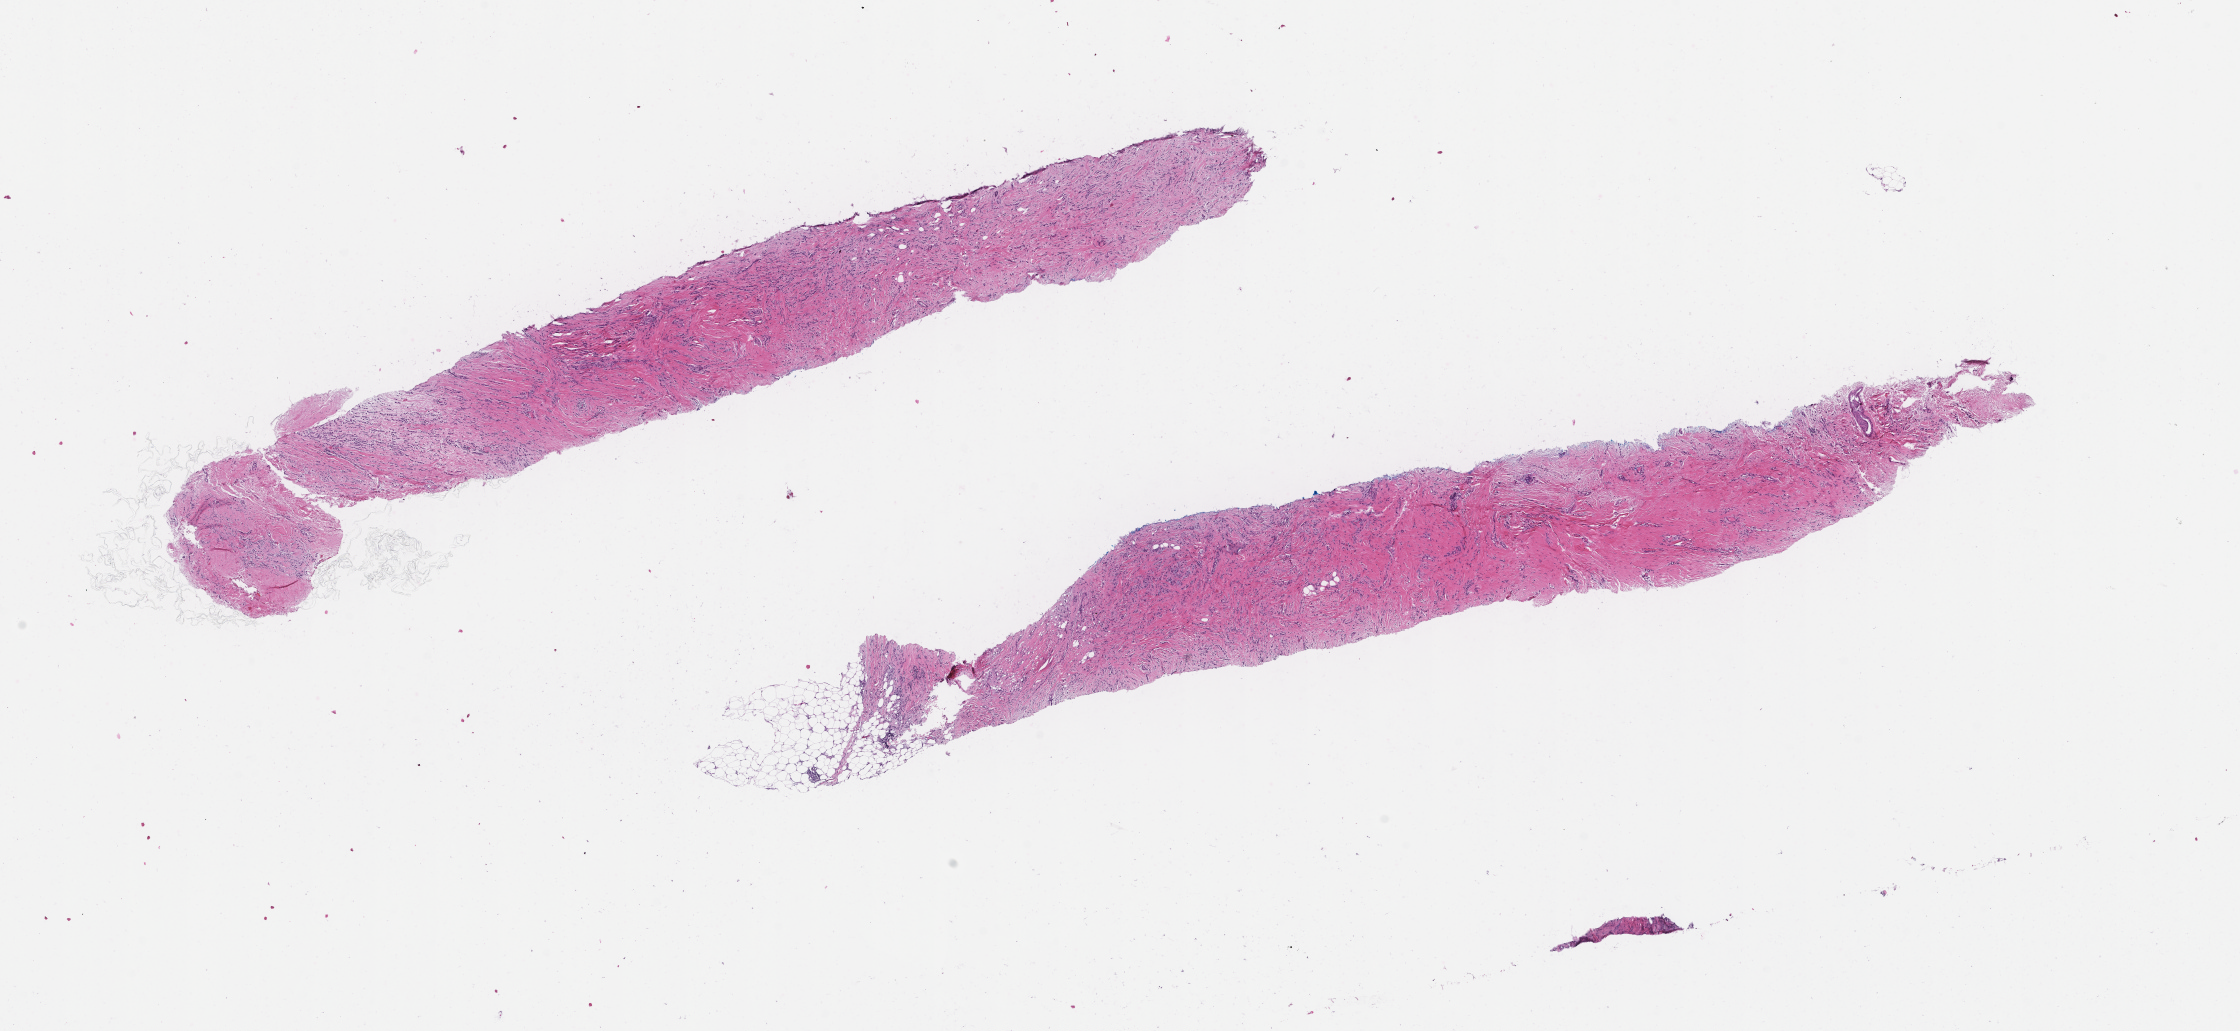
H&E whole-slide image — whole scanned area (about 18.1 x 8.3 mm) shown as a low-resolution overview. Formalin-fixed, paraffin-embedded (FFPE) tissue. Tissue site: breast. Female patient.
This section: primary tumor. Diagnosis: Invasive Breast Carcinoma.